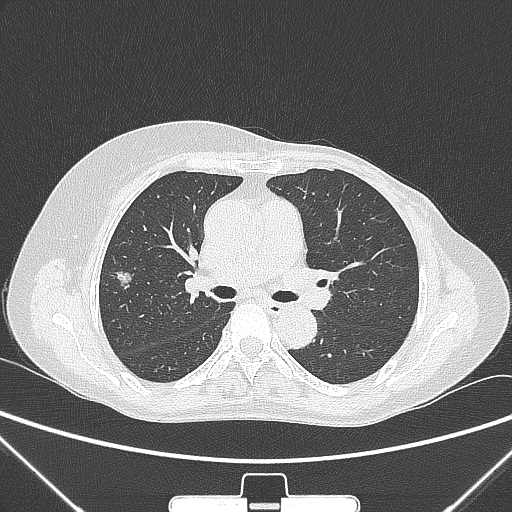
Chest CT, one axial slice. Slice 153 of 265 in the series (ordered by position). Lung window (W 1500 / L -600 HU). 1 mm slice thickness. 512 × 512 image matrix, field of view 350 × 350 mm. Female patient, age 64 years. From the clinical record (not read from this slice): clinical TNM (as recorded): T1c N0 M0; histopathological grade: G1-2.
Outlined on this slice (rectangle marked by the reading radiologist):
- lung tumour (recorded histology: adenocarcinoma): bounding box (x1, y1, x2, y2) in pixels: (110, 265, 140, 297)